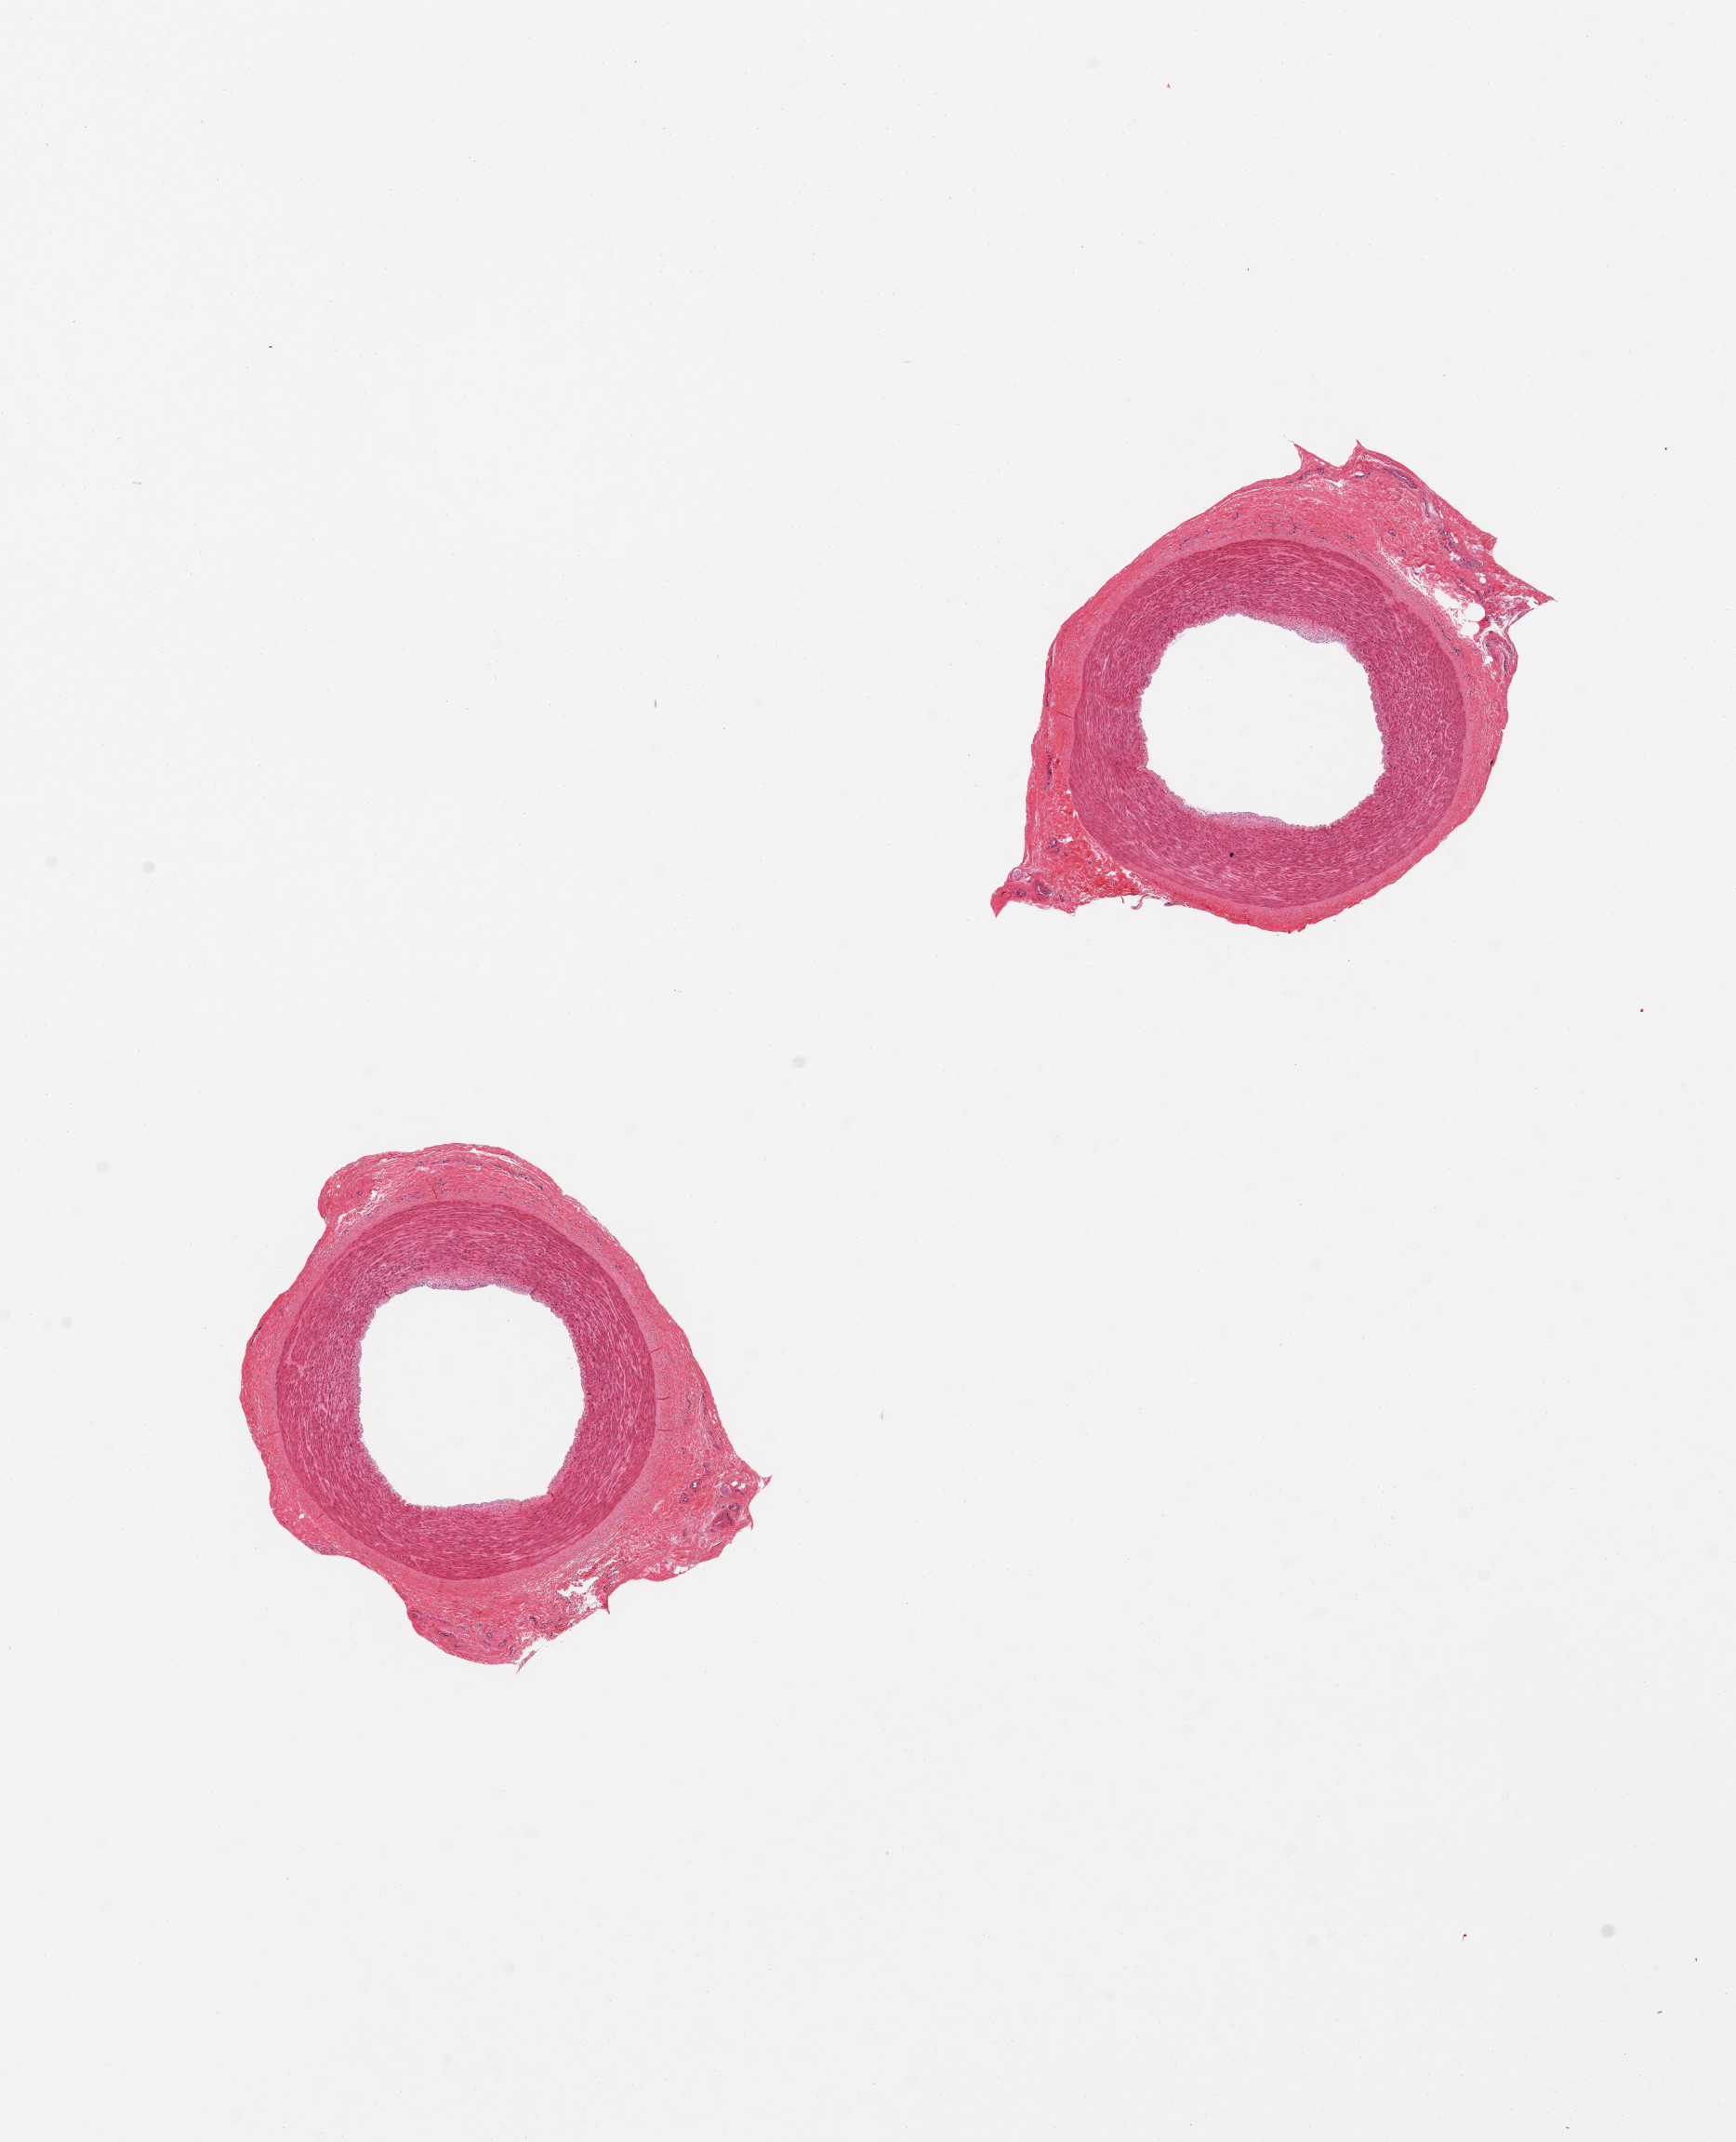
Whole-slide image, H&E stain, low-resolution overview of the scanned area, about 14.8 x 18.2 mm (slide scanned at 20x), PAXgene-fixed paraffin-embedded (PFPE) section, section of tibial artery (target tissue), tissue donor sample. Donor sex: male.
Reviewer comment on this tissue sample: 2 pieces.